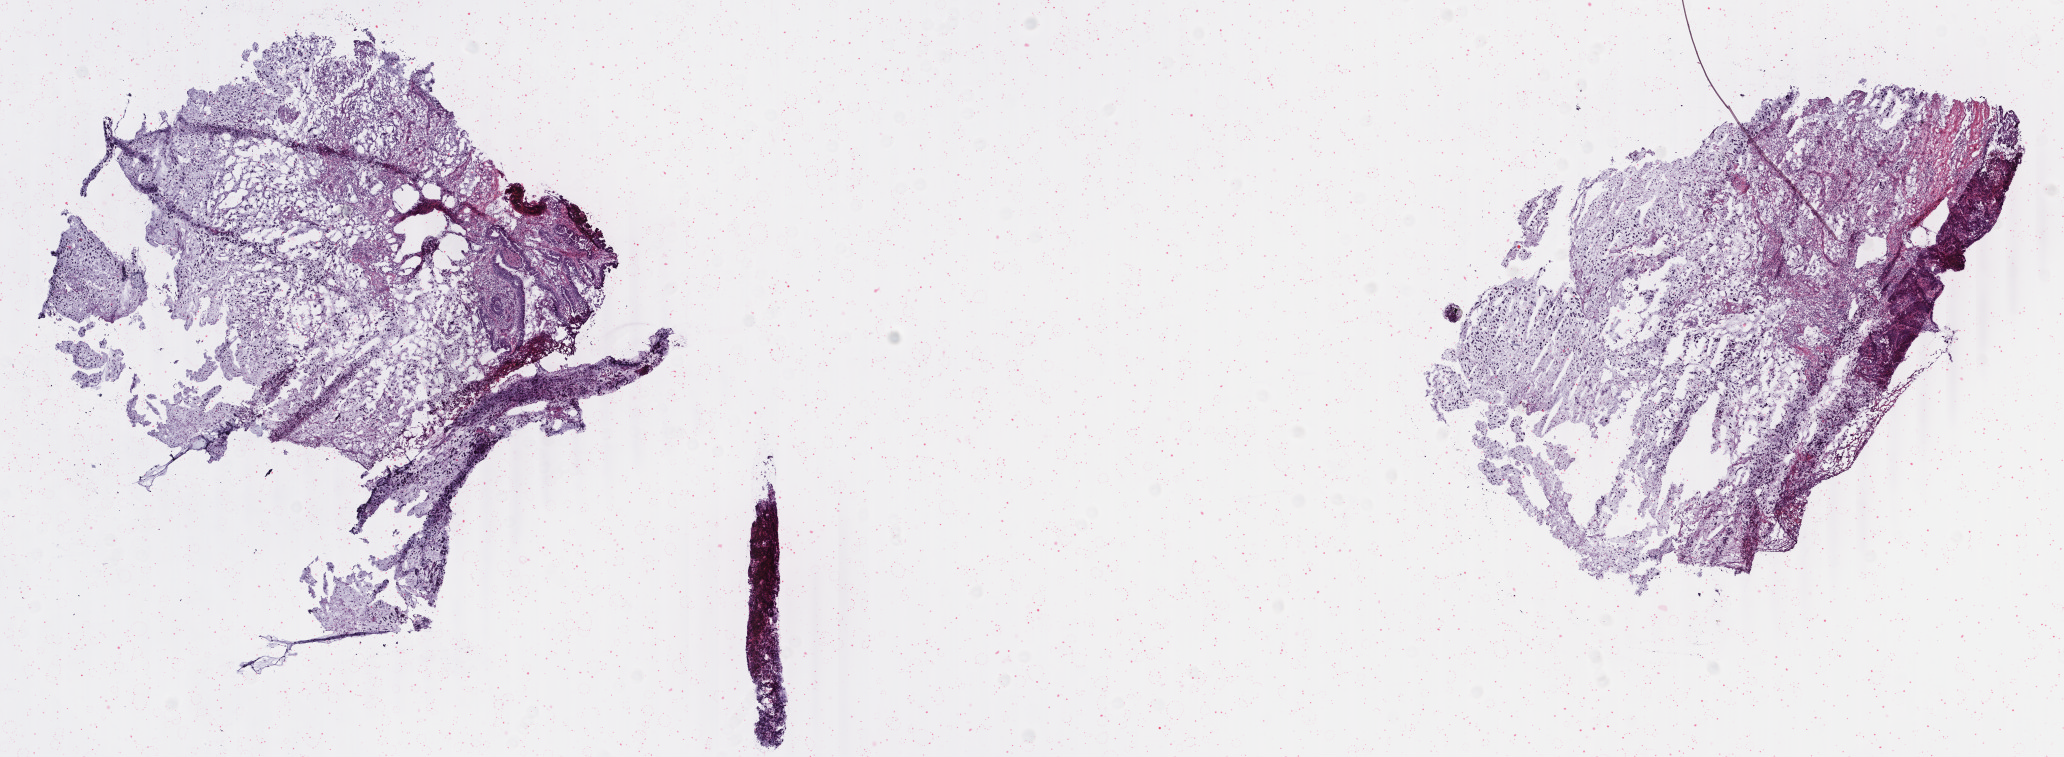
Whole-slide histology image, Hematoxylin and eosin (H&E) stained, low-resolution overview of the scanned area, about 16.4 x 6.0 mm (slide scanned at 40x). Frozen section from the bottom of the tissue portion. Sample: primary tumour, colon. Patient: male, age at initial diagnosis 75 years. Slide review estimates, as recorded: tumour cells 80%, tumour nuclei 75%, normal cells 0%, stromal cells 15%, necrosis 5%. Infiltration values recorded for this section: lymphocyte infiltration 10%, monocyte infiltration 1%, neutrophil infiltration 4%.
- AJCC pathologic stage: IIB
- diagnosis: Mucinous adenocarcinoma (cecum)
- lymph nodes positive (case pathology): 0 of 21 examined